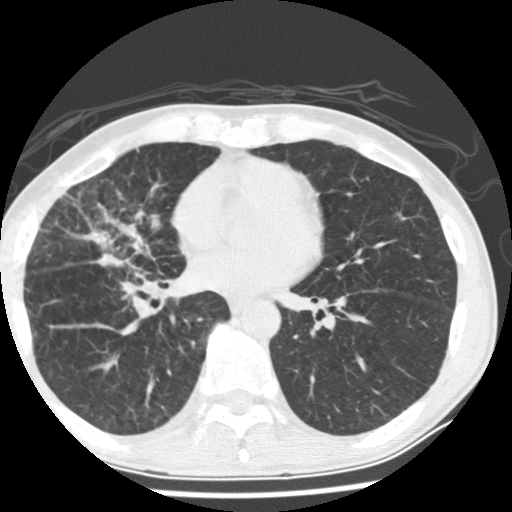
Low-dose screening chest CT, one axial slice. Slice 73 of 162 in the series (ordered by position). Lung window (W 1500 / L -600 HU). 2.5 mm slice thickness. 512 × 512 image matrix.
Structures marked on this image (manually delineated by an expert):
- lesion 1 (tumor, middle lobe of right lung): bounding box (x1, y1, x2, y2) in pixels: (69, 232, 110, 267)